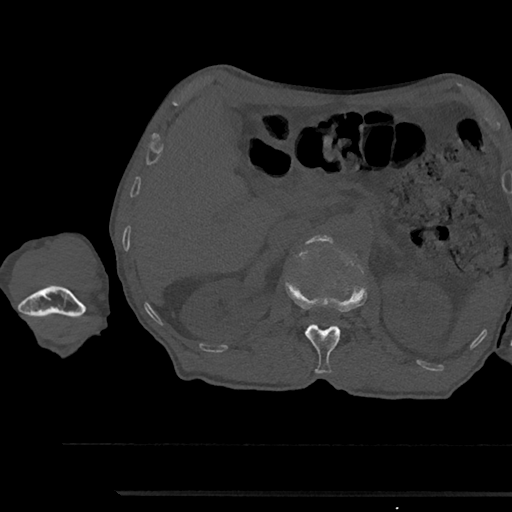
CT including the spine, one axial slice. Position 621 of 797 along the scan axis. Reconstruction kernel Br40s/3. 120 kVp. Bone window (W 1800 / L 400 HU). 0.5 mm slice thickness. 512 × 512 image matrix. Male patient, age 79 years. From the clinical record (not read from this slice): primary cancer: prostate.
Outlined on this slice (semi-automatically segmented with operator editing):
- L1 vertebra: bounding box <286,282,366,374> (left, top, right, bottom; pixels)
- L2 vertebra: <307,235,333,244>